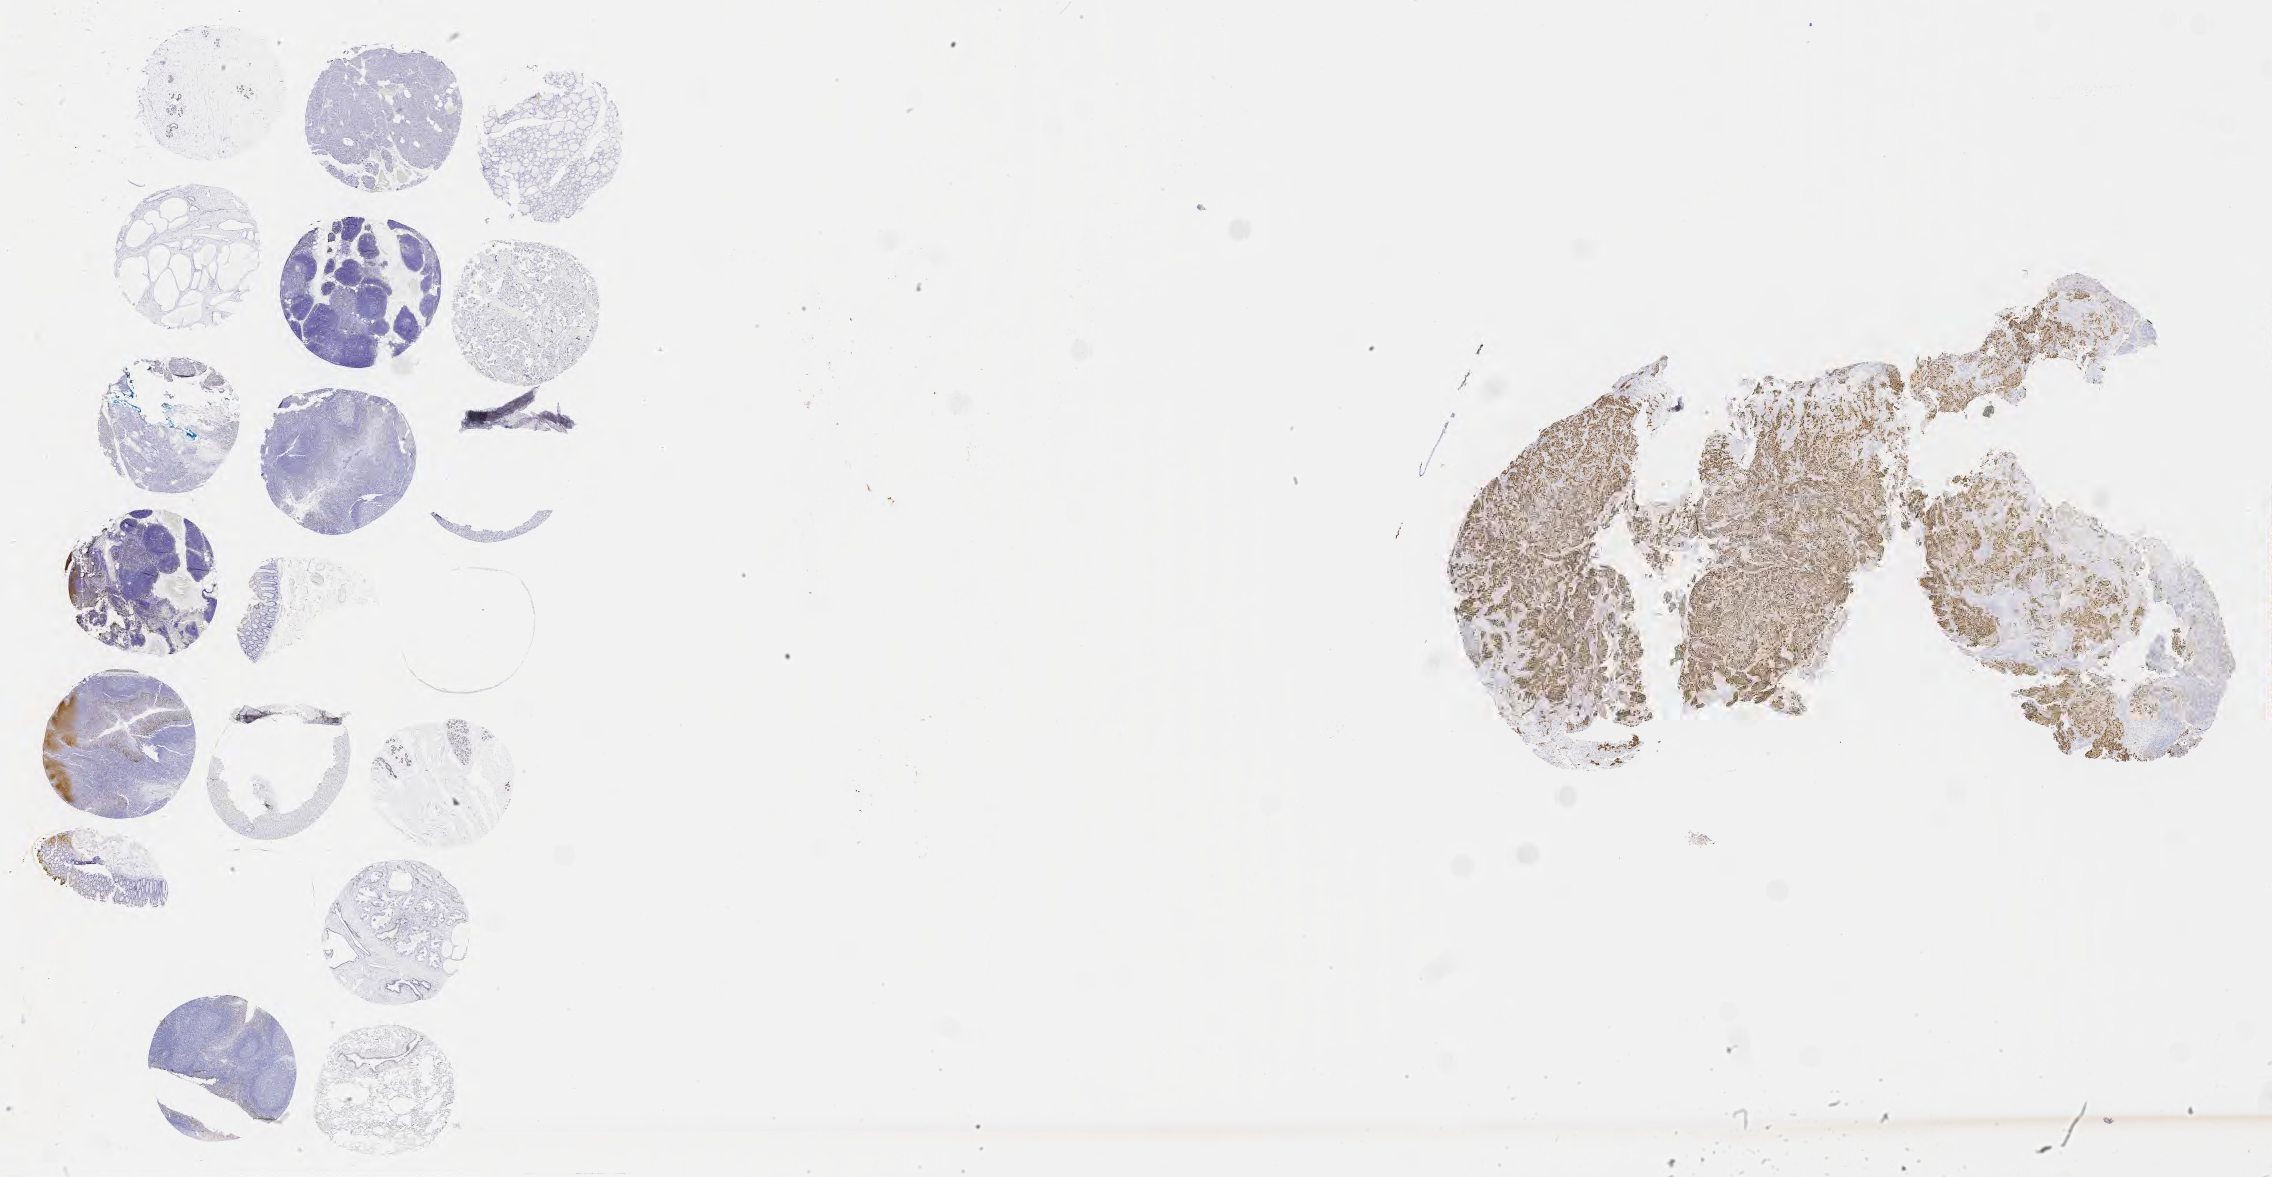
Whole-slide image, immunohistochemical stain for p63 — whole scanned area (about 36.7 x 19.0 mm) shown as a low-resolution overview. Specimen: tumor tissue. Anatomic site: cervix. Patient female; 54 years old.
Diagnosis: Adenocarcinoma, NOS.